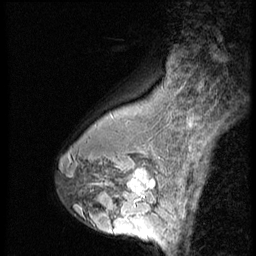
Breast MRI (dynamic contrast-enhanced), one sagittal slice; position 40 of 56 along the scan axis; 3 images stored at this slice position (order not interpretable as contrast timing); 1.5 T; TE 4.2 ms, TR 9 ms; 256 × 256 image matrix, field of view 180 × 180 mm. Female patient, age 43 years. From the clinical record (not read from this slice): setting: breast cancer imaged before/during neoadjuvant chemotherapy; receptor status: HR-positive, HER2-negative.
Structures marked on this image (semi-automatically segmented with operator editing):
- analysis volume of interest (the breast-tissue region the enhancement analysis was run in; not a lesion): bounding box [x1, y1, x2, y2] px = [120, 160, 163, 207]
- tumour enhancement mask (voxels above the 140 % enhancement threshold inside the analysis volume of interest): [125, 170, 156, 207]